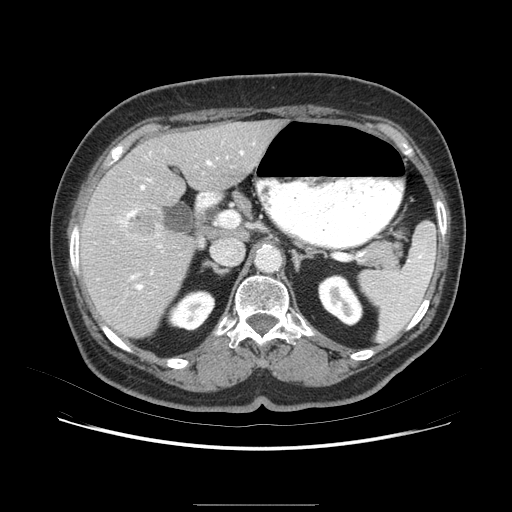
Contrast-enhanced abdominal CT (liver protocol), one axial slice. Slice 43 of 79 in the series (ordered by position). 120 kVp. Soft-tissue window (W 400 / L 40 HU). 2.5 mm slice thickness. 512 × 512 image matrix, field of view 380 × 380 mm. From the clinical record (not read from this slice): diagnosis: hepatocellular carcinoma (patient treated with transarterial chemoembolisation; whether this scan precedes or follows treatment is not stated here); TNM stage (as recorded): Stage-I; Child-Pugh class: A; tumour nodularity: uninodular.
Structures marked on this image (semi-automatically segmented with operator editing):
- liver parenchyma outside the tumour (the mass and vessels are separate outlines, so this box may not span the whole liver): bounding box (x1, y1, x2, y2) in pixels: (78, 122, 290, 344)
- mass: (123, 202, 169, 245)
- liver vessels: (98, 146, 263, 324)